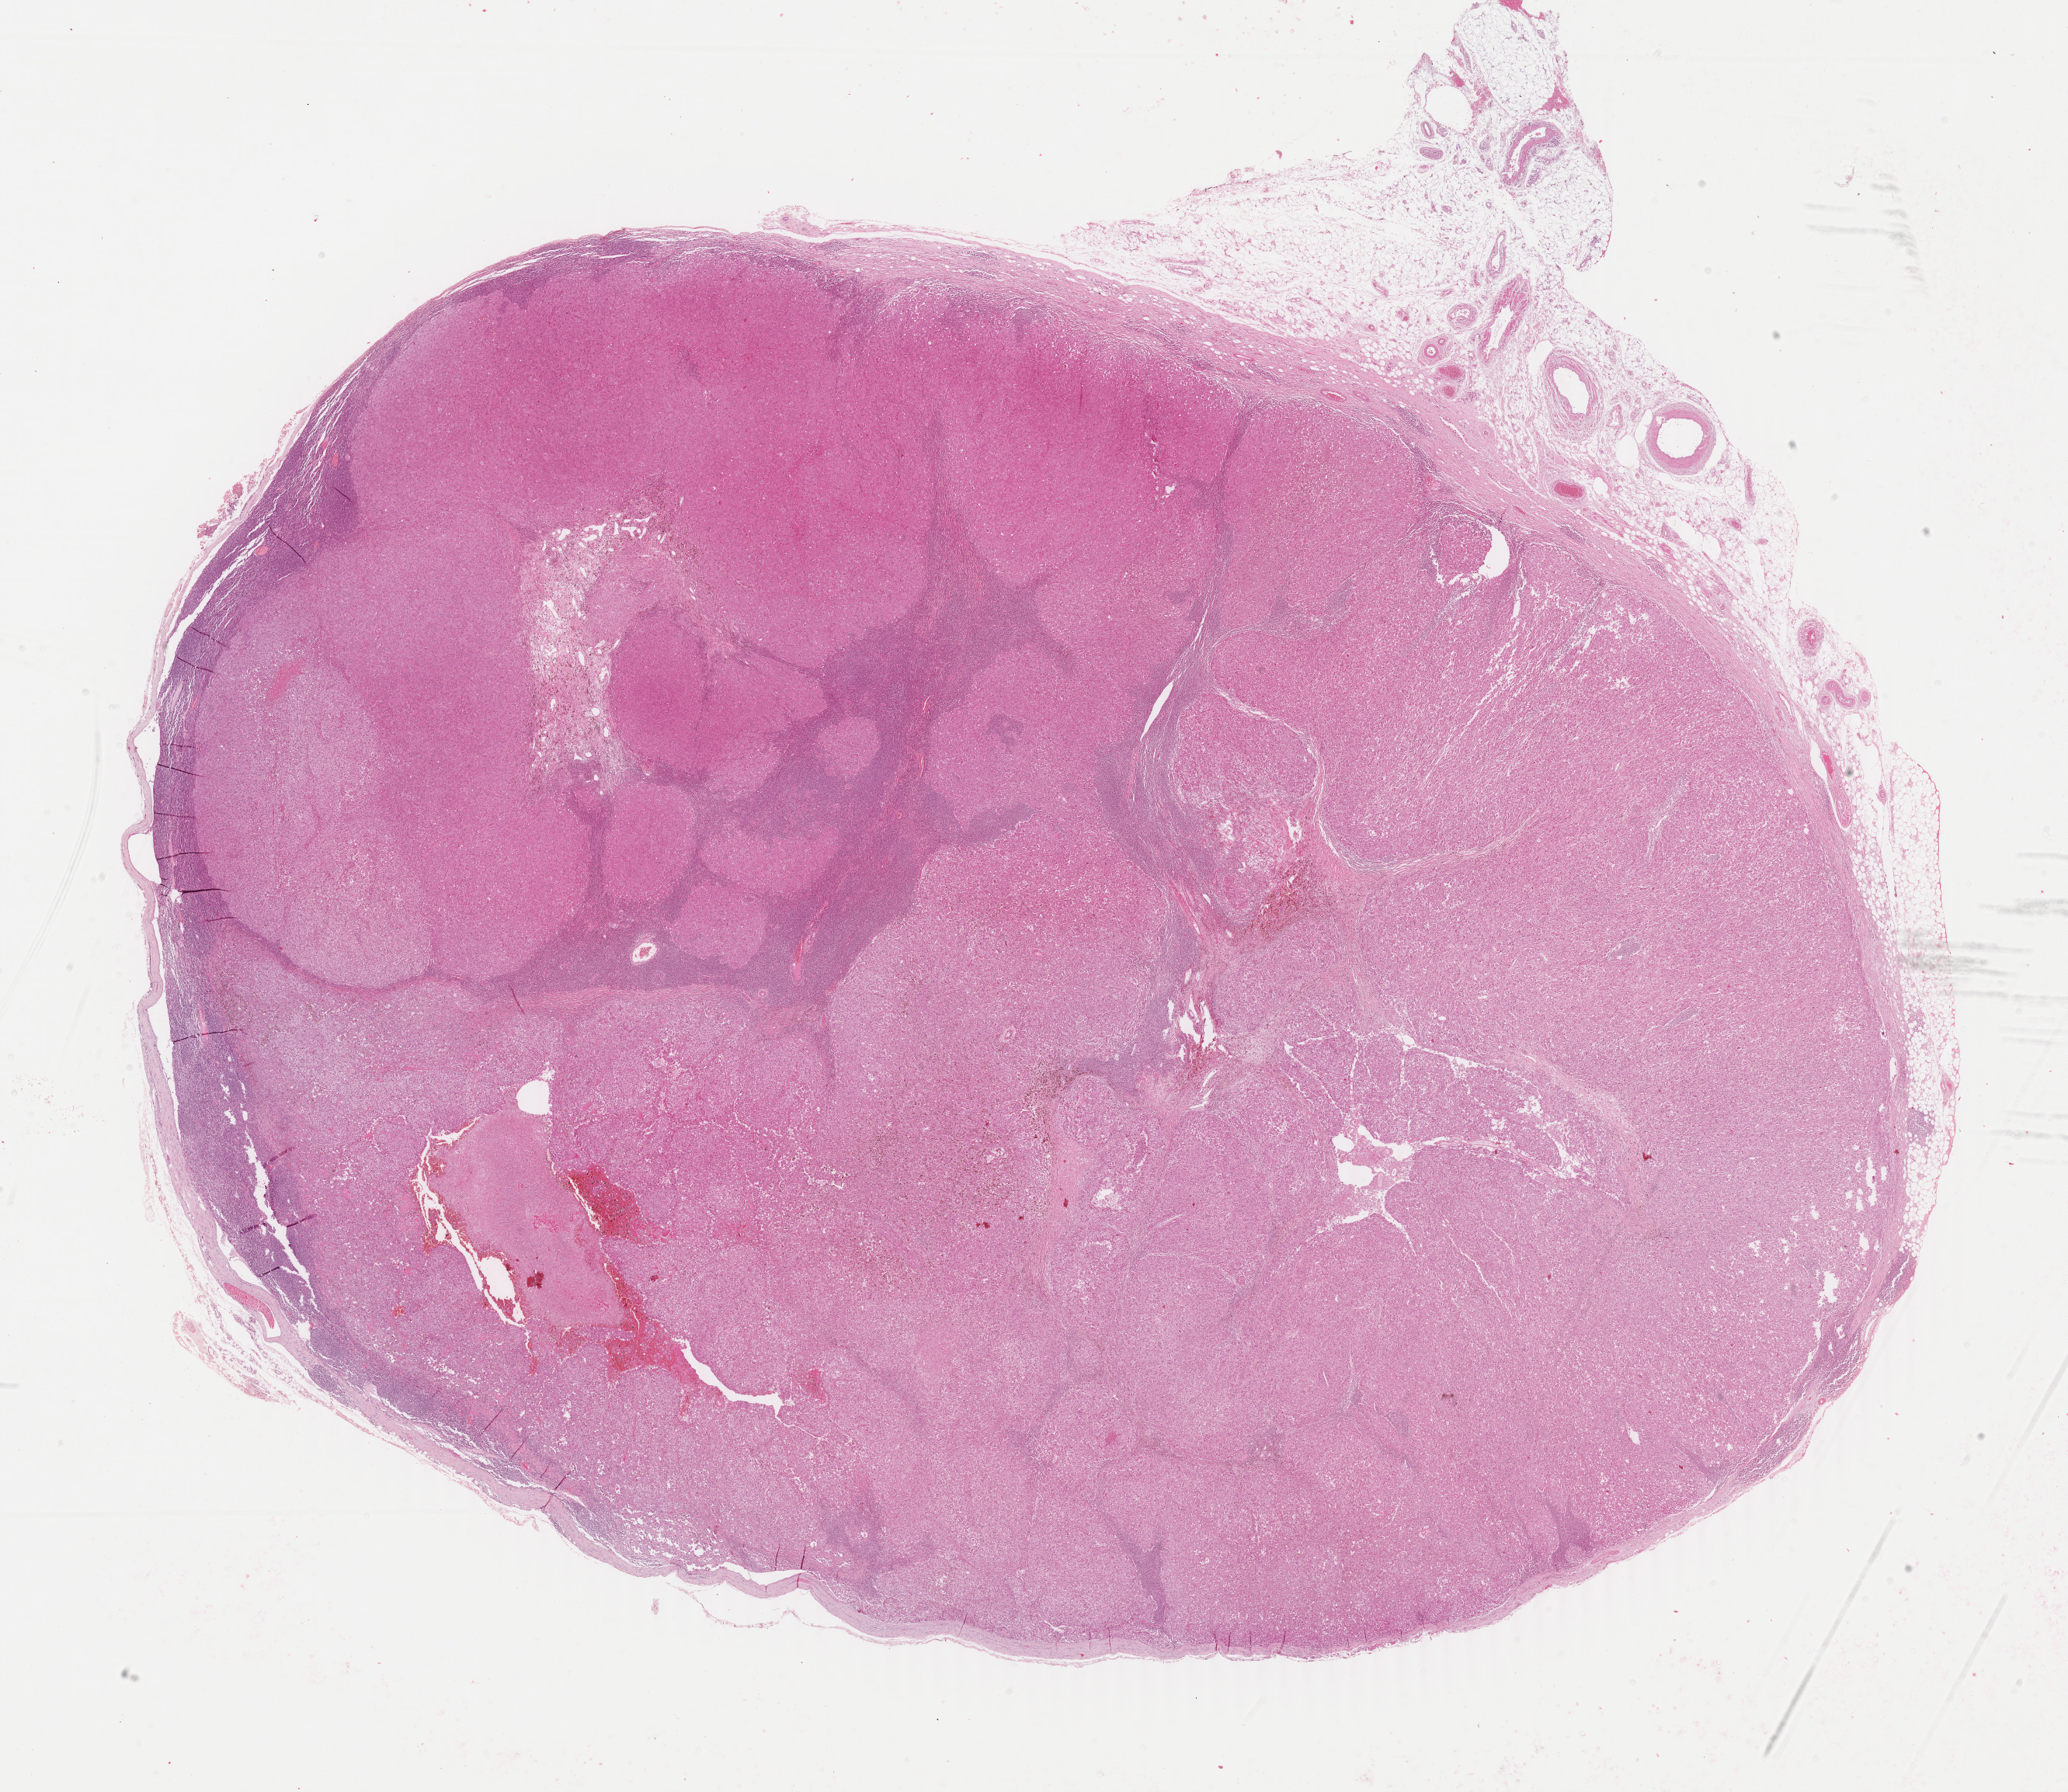
H&E-stained whole-slide image, whole scanned area (about 21.2 x 18.4 mm) shown as a low-resolution overview; formalin-fixed paraffin-embedded (FFPE) diagnostic section; primary tumour sample from the skin. Patient: male, age at initial diagnosis 78 years.
Histologic diagnosis: Malignant melanoma, NOS.